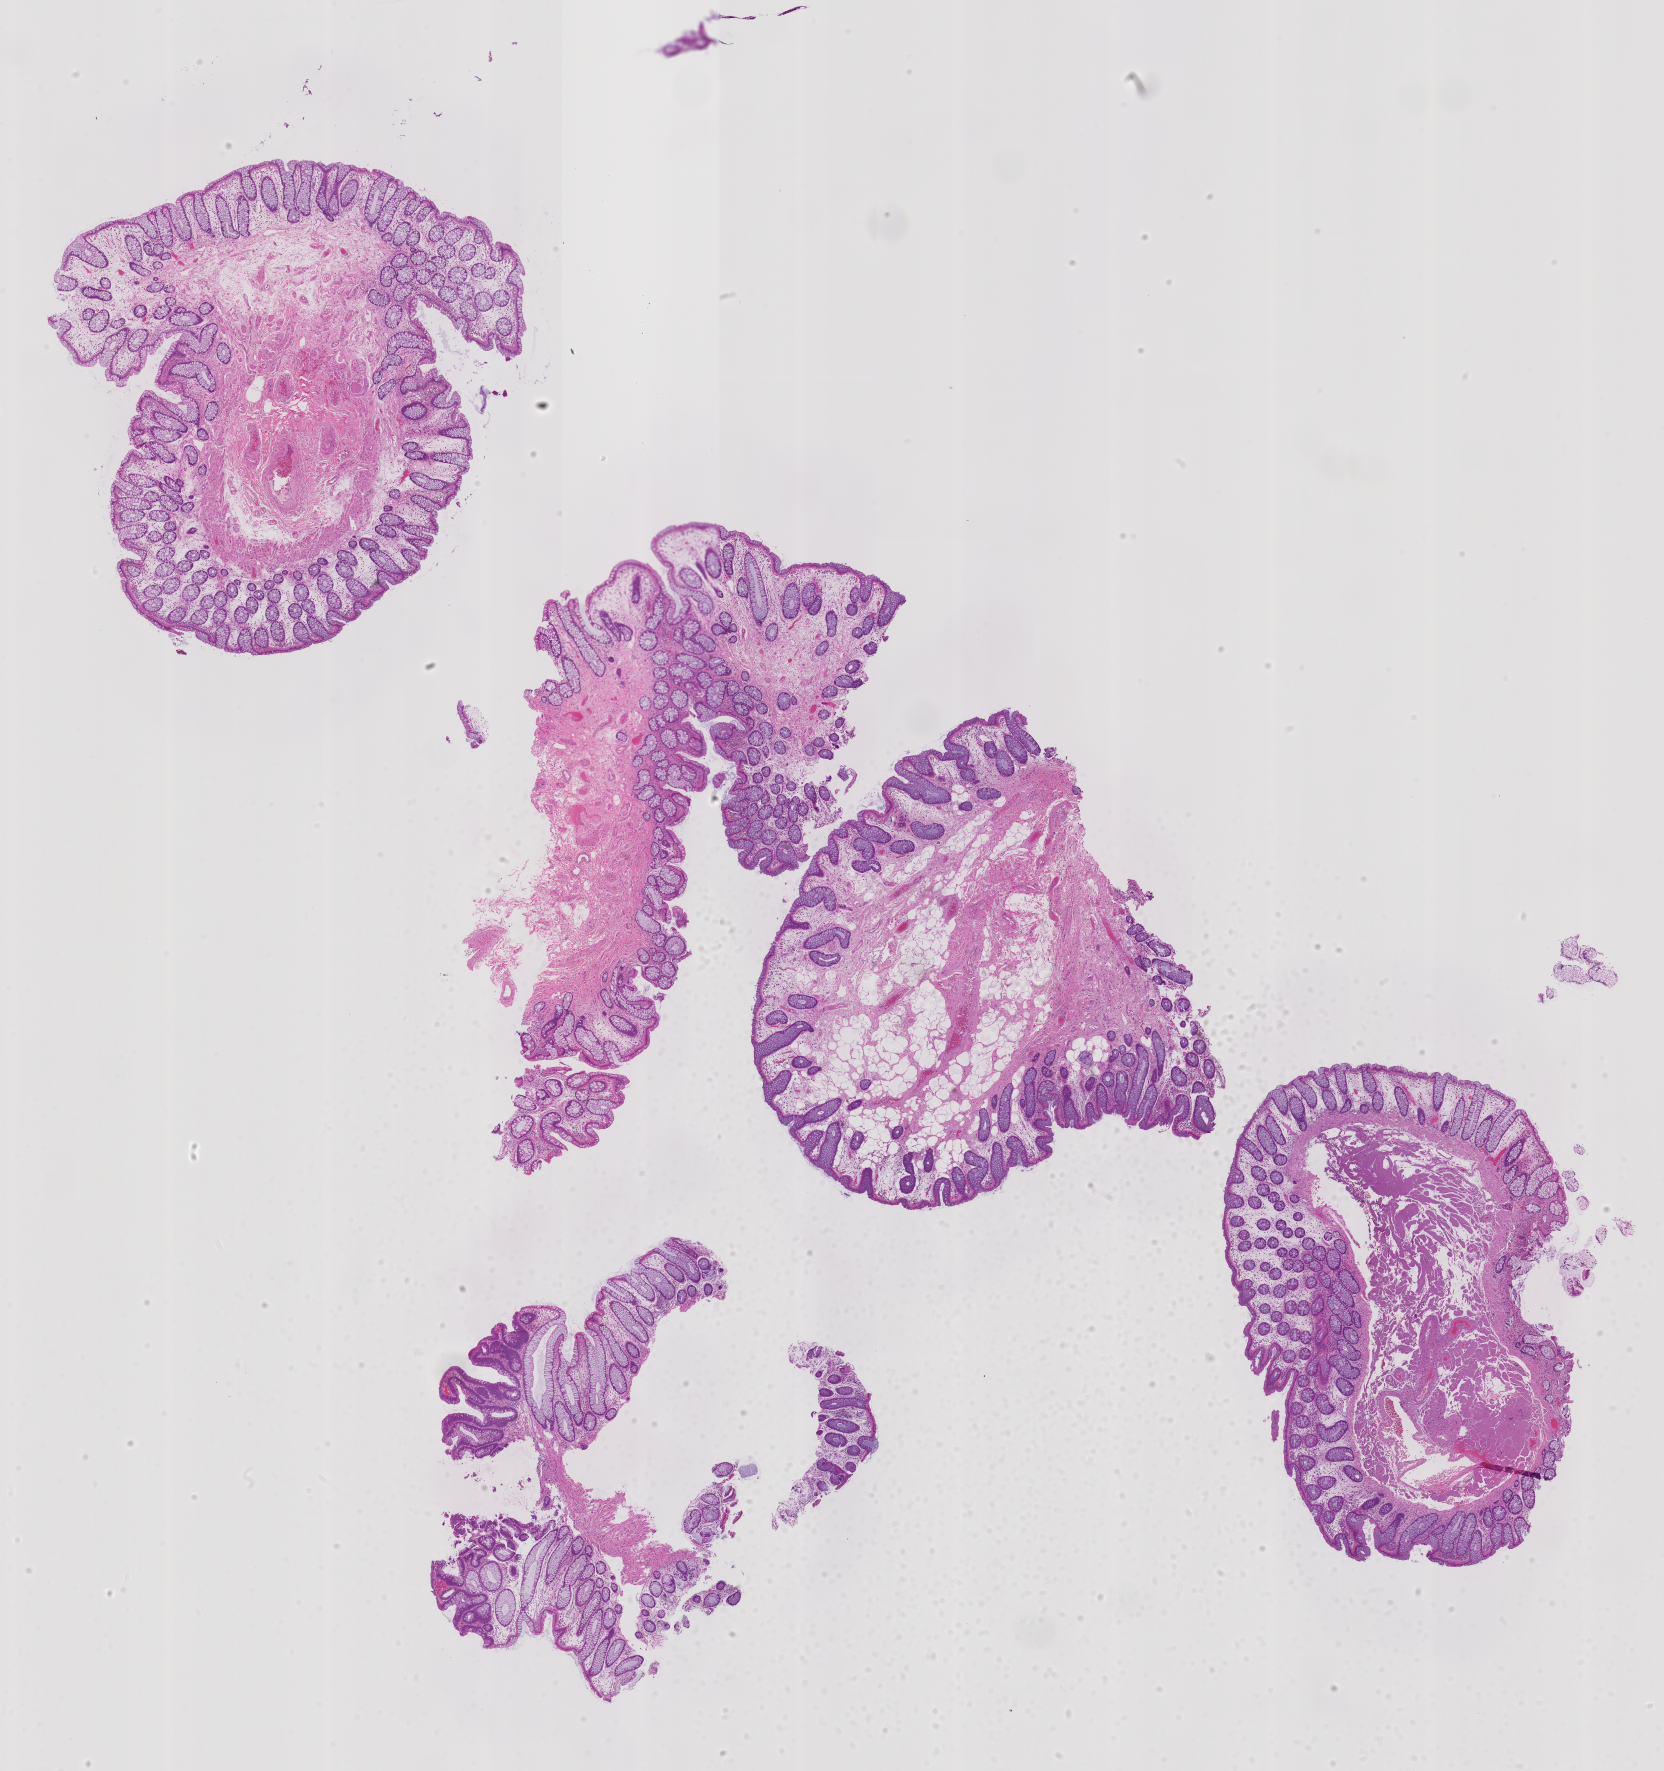
Whole-slide image, H&E stain: colon biopsy, a low-resolution overview of the entire scanned area, about 13.3 x 14.2 mm. Patient sex: female.
* specimen: formalin-fixed paraffin-embedded section; site: sigmoid colon